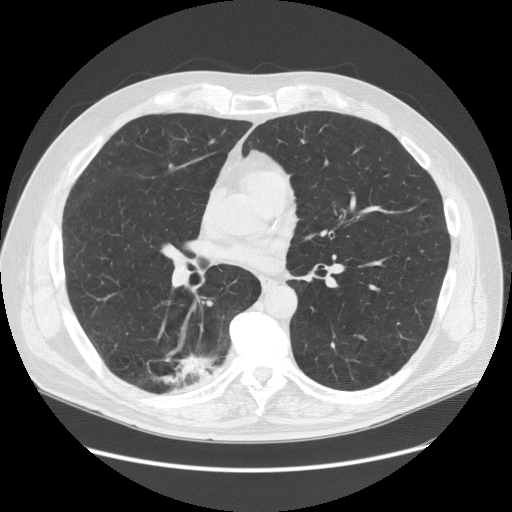
Chest CT (low-dose screening protocol), one axial image, baseline annual screen, lung window (W 1500 / L -600 HU), 2.5 mm slice thickness, standard (soft-tissue) reconstruction kernel (STANDARD), 120 kVp, 512 × 512 image matrix, field of view 400 × 400 mm. Male, age 68 years at enrolment.
Lesion marked by an expert reader, bounding box <127,340,226,412> (left, top, right, bottom; pixels). Screening reader's record for this exam (one nodule recorded; not confirmed to be the boxed lesion): non-calcified nodule or mass ≥4 mm, right lower lobe, 37 × 20 mm, spiculated (stellate) margins, soft tissue attenuation. Official screen result: positive, change unspecified: nodule(s) >= 4 mm or enlarging nodule(s), mass(es), or other non-specific abnormalities suspicious for lung cancer. Lung cancer was diagnosed 24 days after this screen: adenosquamous carcinoma, right lower lobe, poorly differentiated (G3), stage IIIA (AJCC 6th edition), 30 mm at pathology.